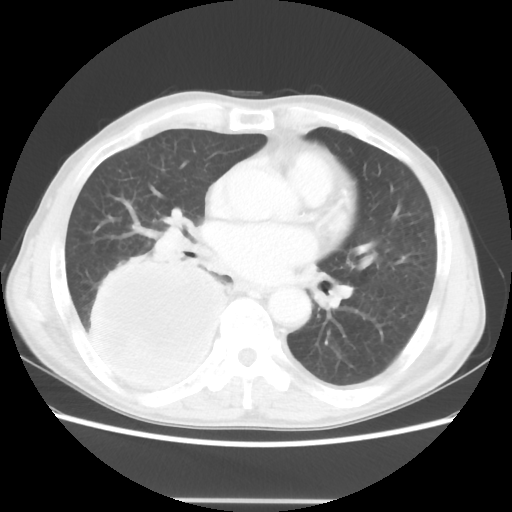
Chest CT, one axial slice. Position 22 of 48 along the scan axis. Reconstruction kernel STANDARD. 100 kVp. Lung window (W 1500 / L -600 HU). 5 mm slice thickness. 512 × 512 image matrix, field of view 361 × 361 mm. Male patient, age 66 years. Case-level facts recorded for this patient, not image findings: clinical TNM (as recorded): T4 N1 M1; histopathological grade: G3.
Structures marked on this image (bounding box drawn by a radiologist):
- lung tumour (recorded histology: small cell carcinoma): box from (x=75, y=246) to (x=225, y=400) px